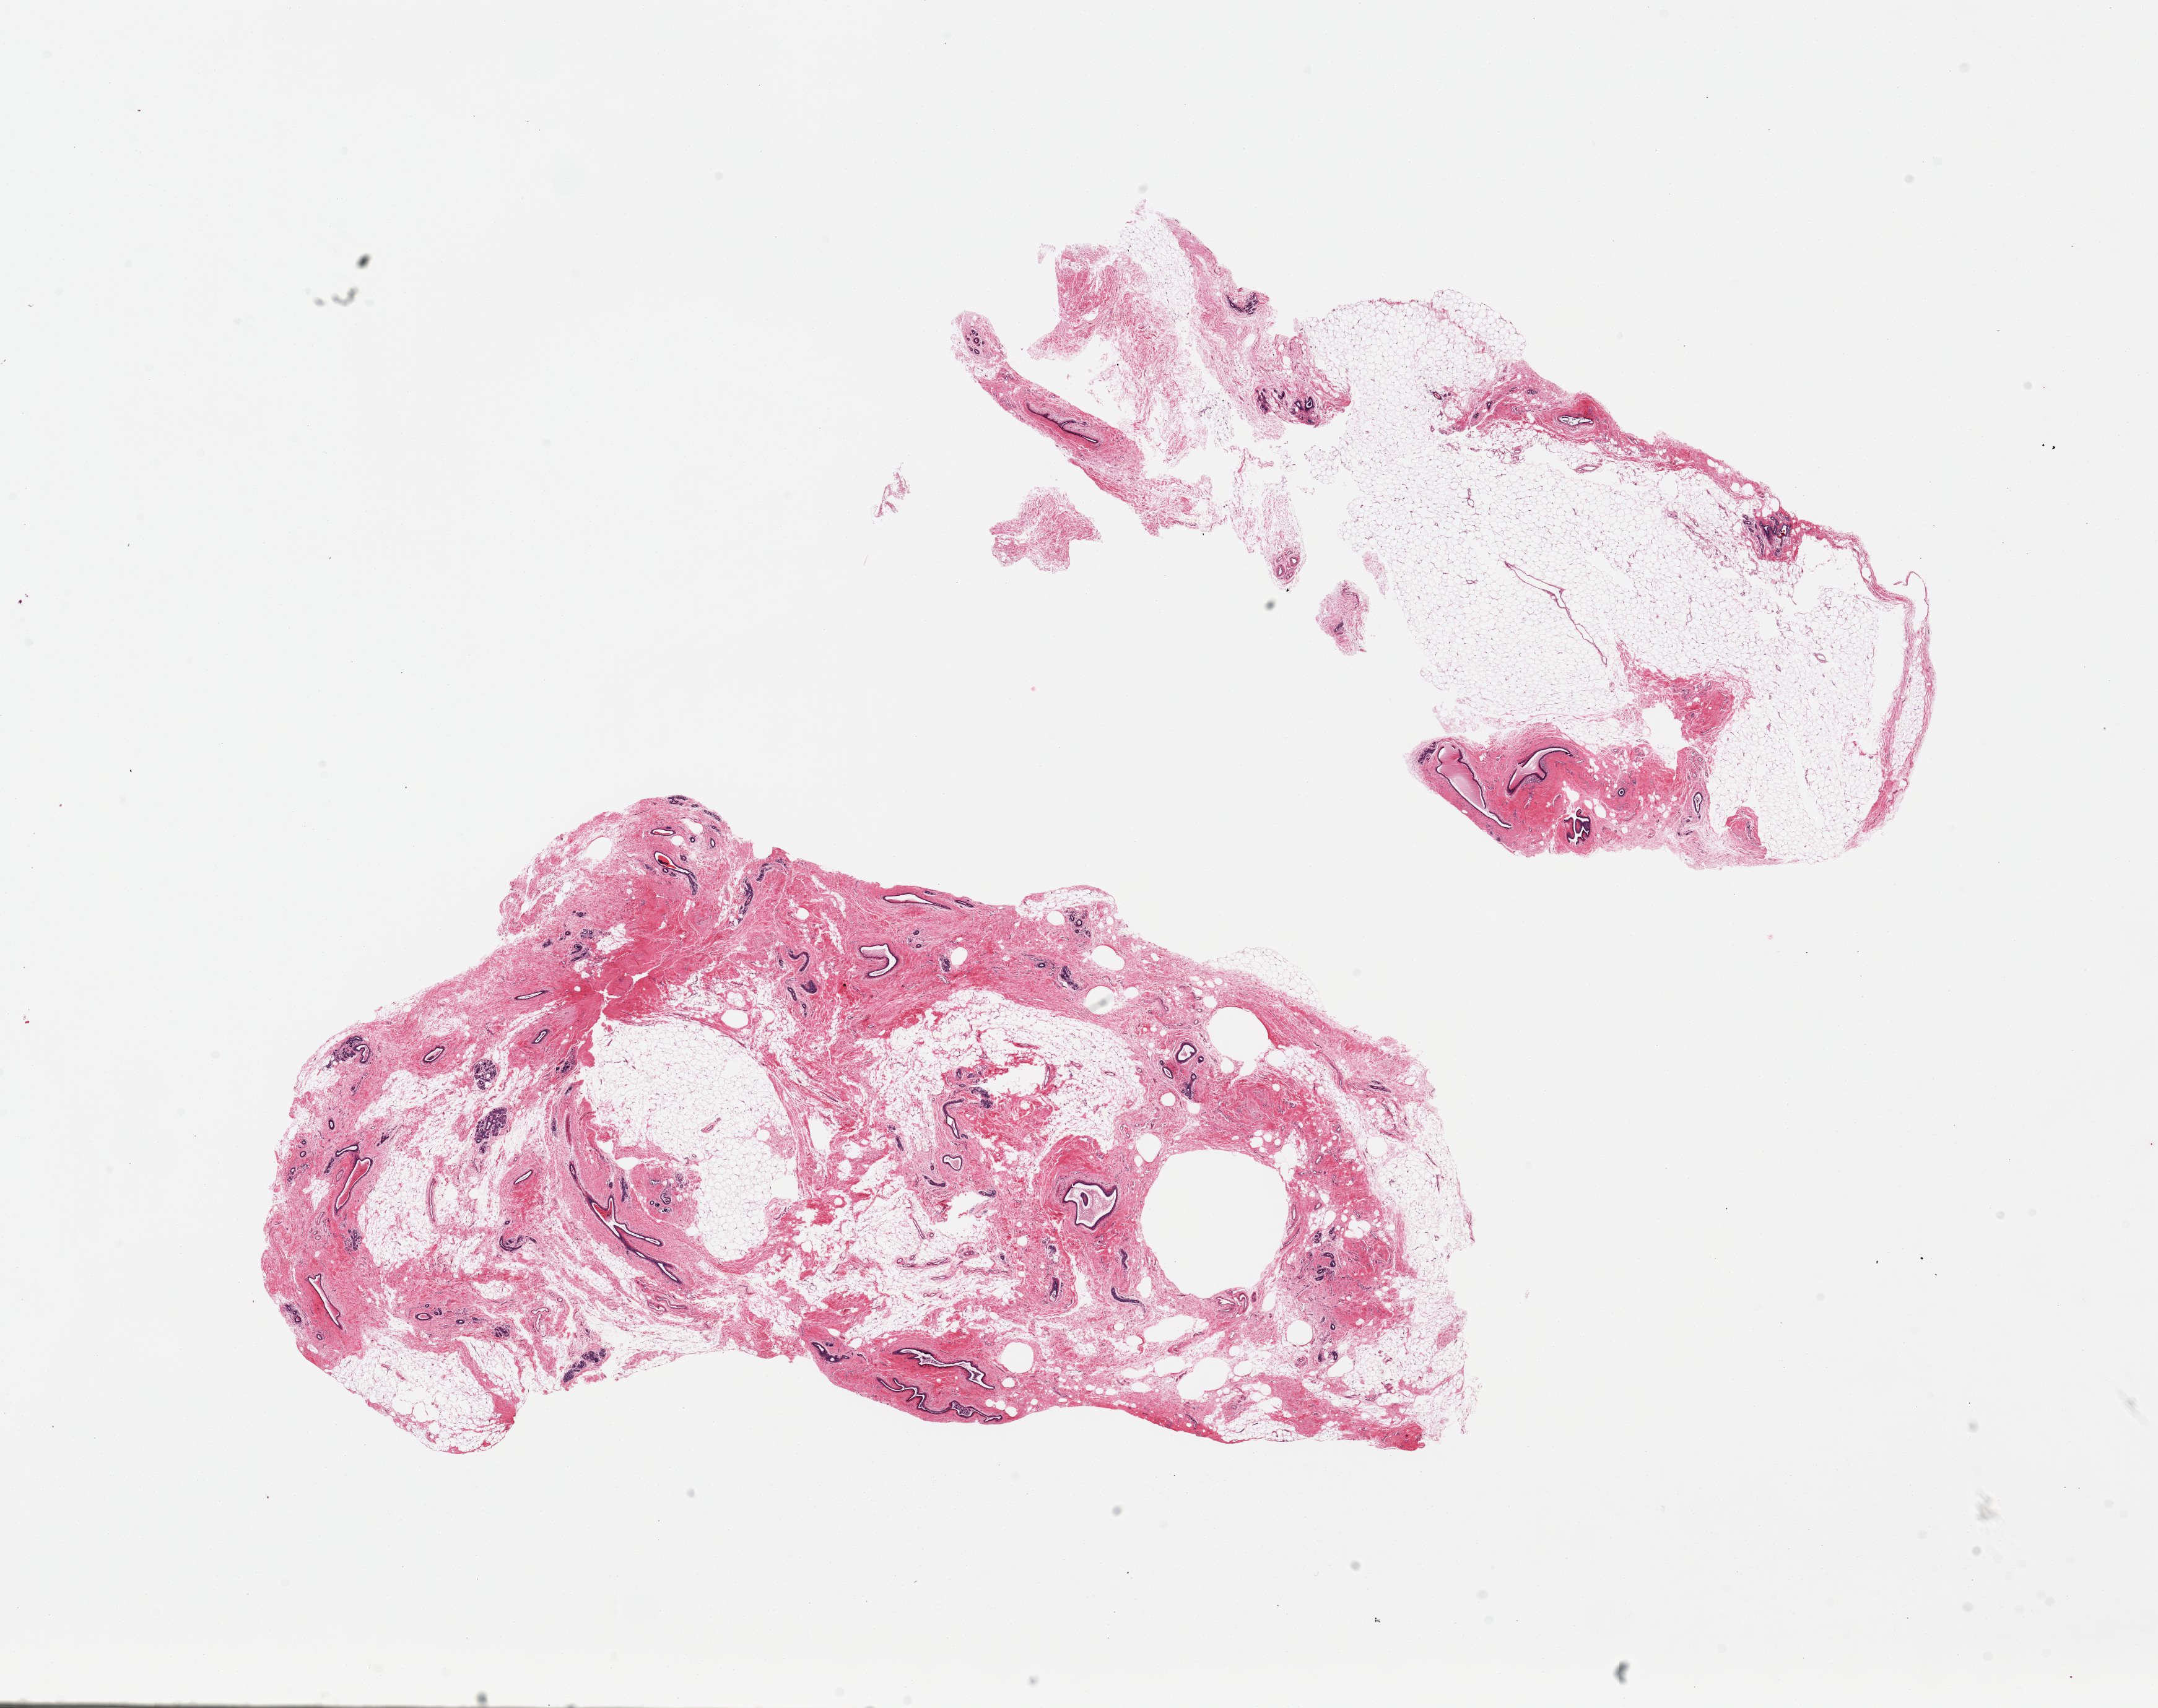
Haematoxylin and eosin whole-slide image — a low-resolution overview of the entire scanned area, about 27.6 x 21.8 mm (from a 20x scan). PAXgene-fixed paraffin-embedded (PFPE) section. Section of breast (target tissue). Tissue donor sample. Donor sex: female.
Reviewer comment on this tissue sample: 2 pieces. 16x9 & 14x6mm; Ducts and lobules present. Larger piece good; smaller is mainly adipose.